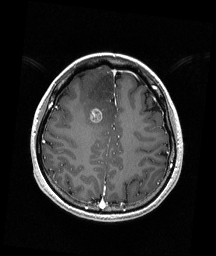
Brain MRI from a brain-tumour surgery series, one axial slice; slice 59 of 192 in the series (ordered by position); T1-weighted post-contrast; 216 × 256 image matrix, field of view 211 × 250 mm. Case-level facts recorded for this patient, not image findings: histopathology: Astrocytoma; WHO grade: 4; IDH mutation: yes; tumour location: Right Frontal.
Annotated regions visible in this slice (outlined manually by an expert reader):
- tumour: bounding box (x1, y1, x2, y2) in pixels: (90, 107, 102, 123)